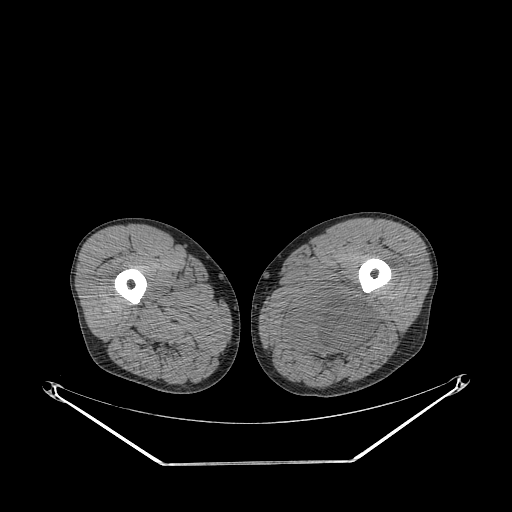
CT of an extremity soft-tissue mass (from a PET/CT study), one axial slice. Reconstruction kernel STANDARD. 140 kVp. Soft-tissue window (W 400 / L 40 HU). 3.75 mm slice thickness. 512 × 512 image matrix, field of view 500 × 500 mm. Male patient. Case-level facts recorded for this patient, not image findings: histological type: undifferentiated pleomorphic liposarcoma; grade: high; site of the primary tumour: left thigh.
Structures marked on this image (expert contour drawn on MRI and transferred to this co-registered scan by the dataset authors):
- gross tumour volume including surrounding oedema: bounding box <281,288,375,359> (left, top, right, bottom; pixels)
- gross tumour volume (mass): <290,290,373,350>